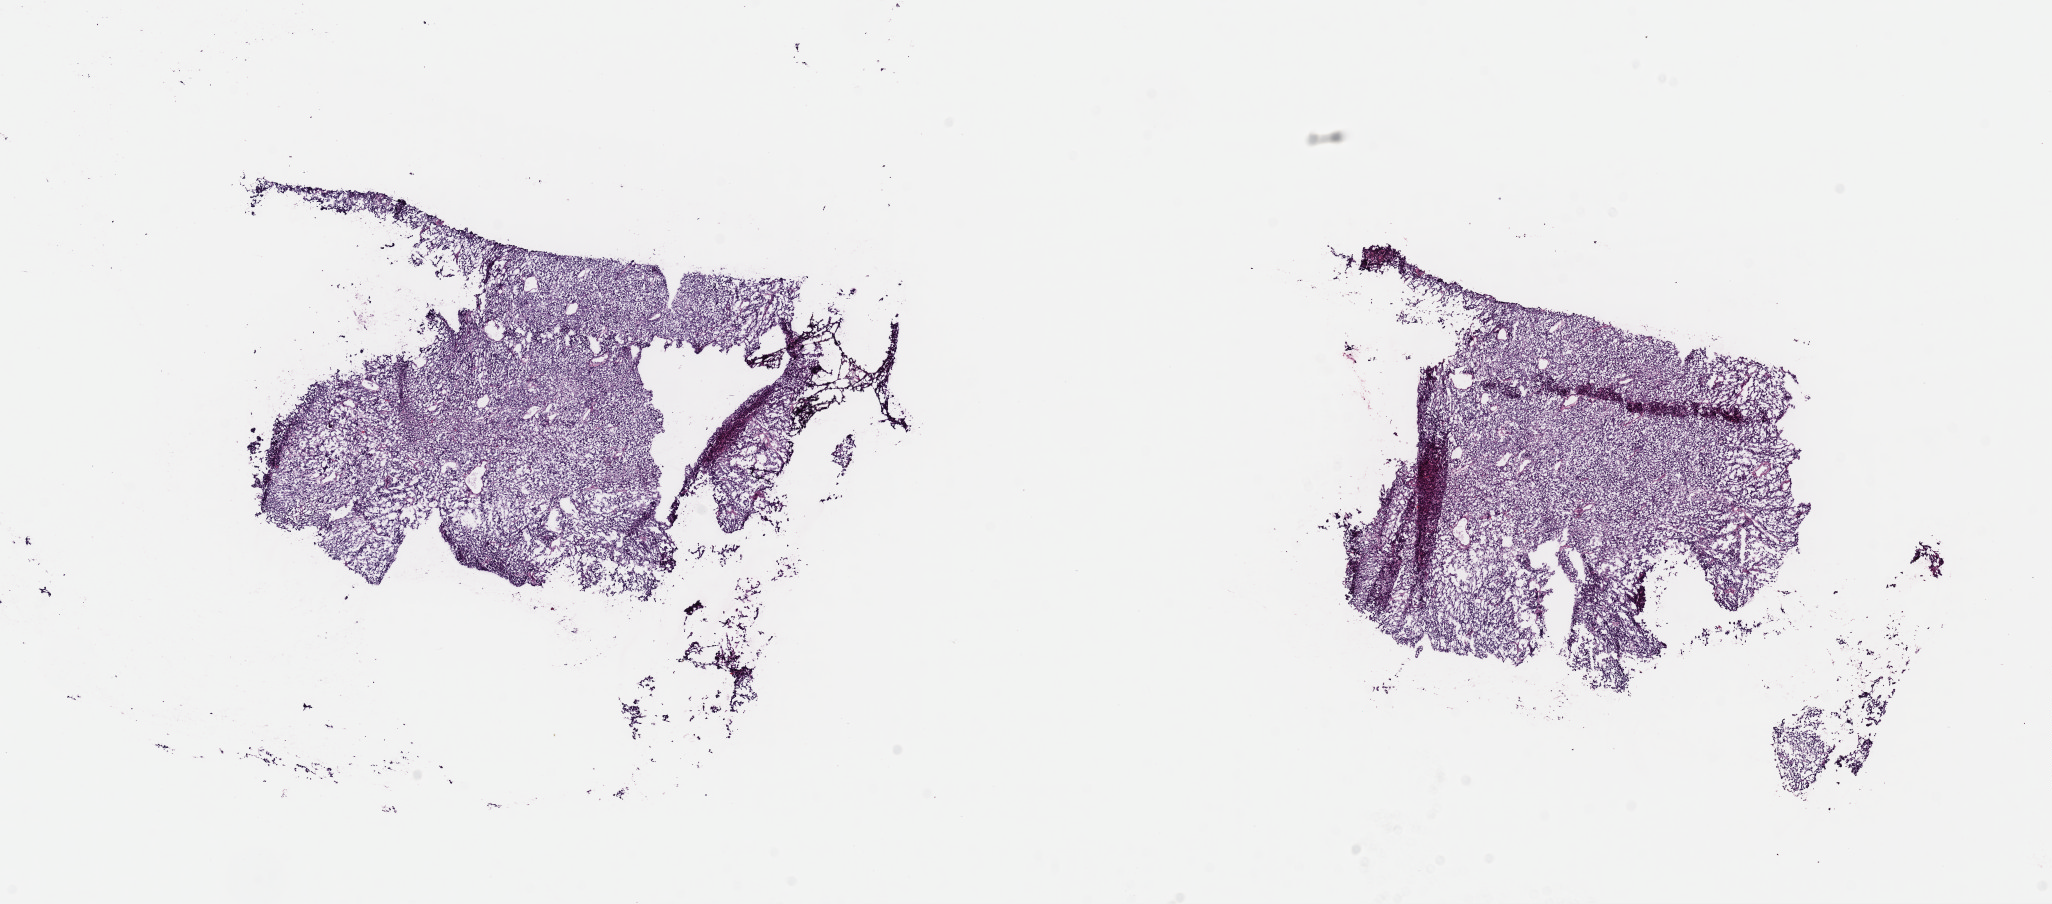
Hematoxylin and eosin (H&E) stained whole-slide image — low-resolution overview of the scanned area, about 16.2 x 7.1 mm (from a 40x scan); frozen section from the top of the tissue portion; metastatic tumour sample, sampled site: lymph nodes of axilla or arm. Male, age 72 years at initial diagnosis. Pathologist review of this section (percent, as recorded): tumour cells 80%, tumour nuclei 80%, normal cells 0%, stromal cells 18%, necrosis 2%. Inflammatory infiltration, as recorded: lymphocyte infiltration 5%, monocyte infiltration 2%, neutrophil infiltration 0%.
This section: metastatic tumour tissue. Patient diagnosis: Malignant melanoma, NOS.